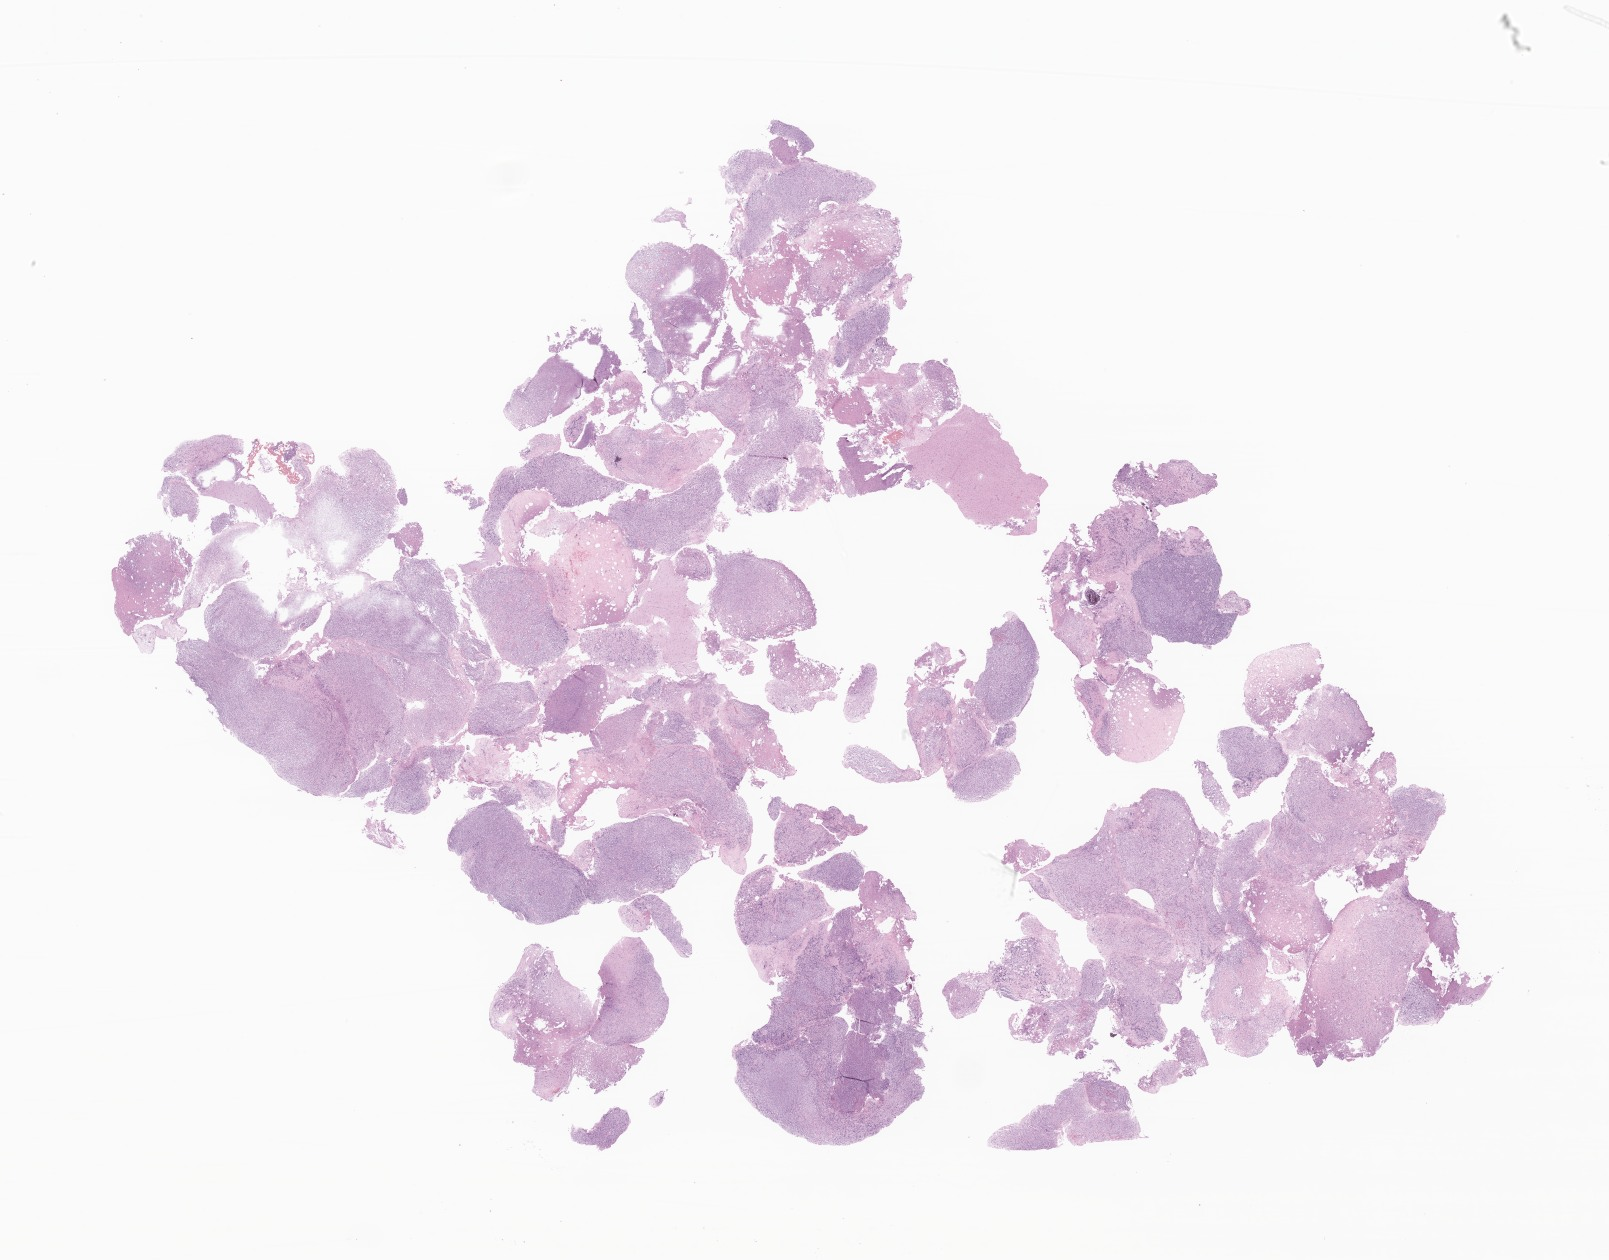
Digitized H&E-stained section of tumor tissue from the brain — shown as a low-resolution overview of the whole scanned area (about 27.1 x 21.3 mm); formalin-fixed, paraffin-embedded (FFPE) tissue. Patient male; age 956 days (about 2.6 years).
Recorded diagnosis: Neoplasm, uncertain whether benign or malignant.